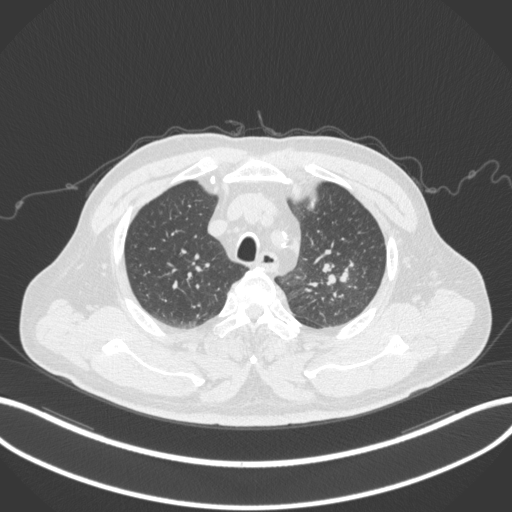
Chest CT, one axial slice; position 243 of 286 along the scan axis; reconstruction kernel B31f; lung window (W 1500 / L -600 HU); 512 × 512 image matrix, field of view 400 × 400 mm. Male patient, age 67 years. Case-level facts recorded for this patient, not image findings: clinical TNM (as recorded): T2a N1 M0; histopathological grade: G3.
Annotated regions visible in this slice (rectangle marked by the reading radiologist):
- lung tumour (recorded histology: adenocarcinoma): bounding box [x1, y1, x2, y2] px = [319, 257, 350, 286]